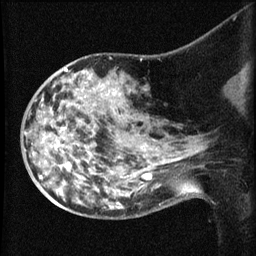
Breast MRI (dynamic contrast-enhanced), one sagittal slice; position 35 of 60 along the scan axis; dynamic contrast-enhanced series, image 2 of 3 at this slice position (ordered by acquisition); 1.5 T; TE 4.2 ms, TR 8.2 ms; 2.1 mm slice thickness; 256 × 256 image matrix, field of view 180 × 180 mm. Patient: female, 50 years.
Annotated regions visible in this slice (semi-automatically segmented with operator editing):
- analysis volume of interest (the breast-tissue region the enhancement analysis was run in; not a lesion): box from (x=38, y=74) to (x=169, y=211) px
- tumour enhancement mask (voxels above the 70 % enhancement threshold inside the analysis volume of interest): (x=40, y=147)–(x=147, y=179)